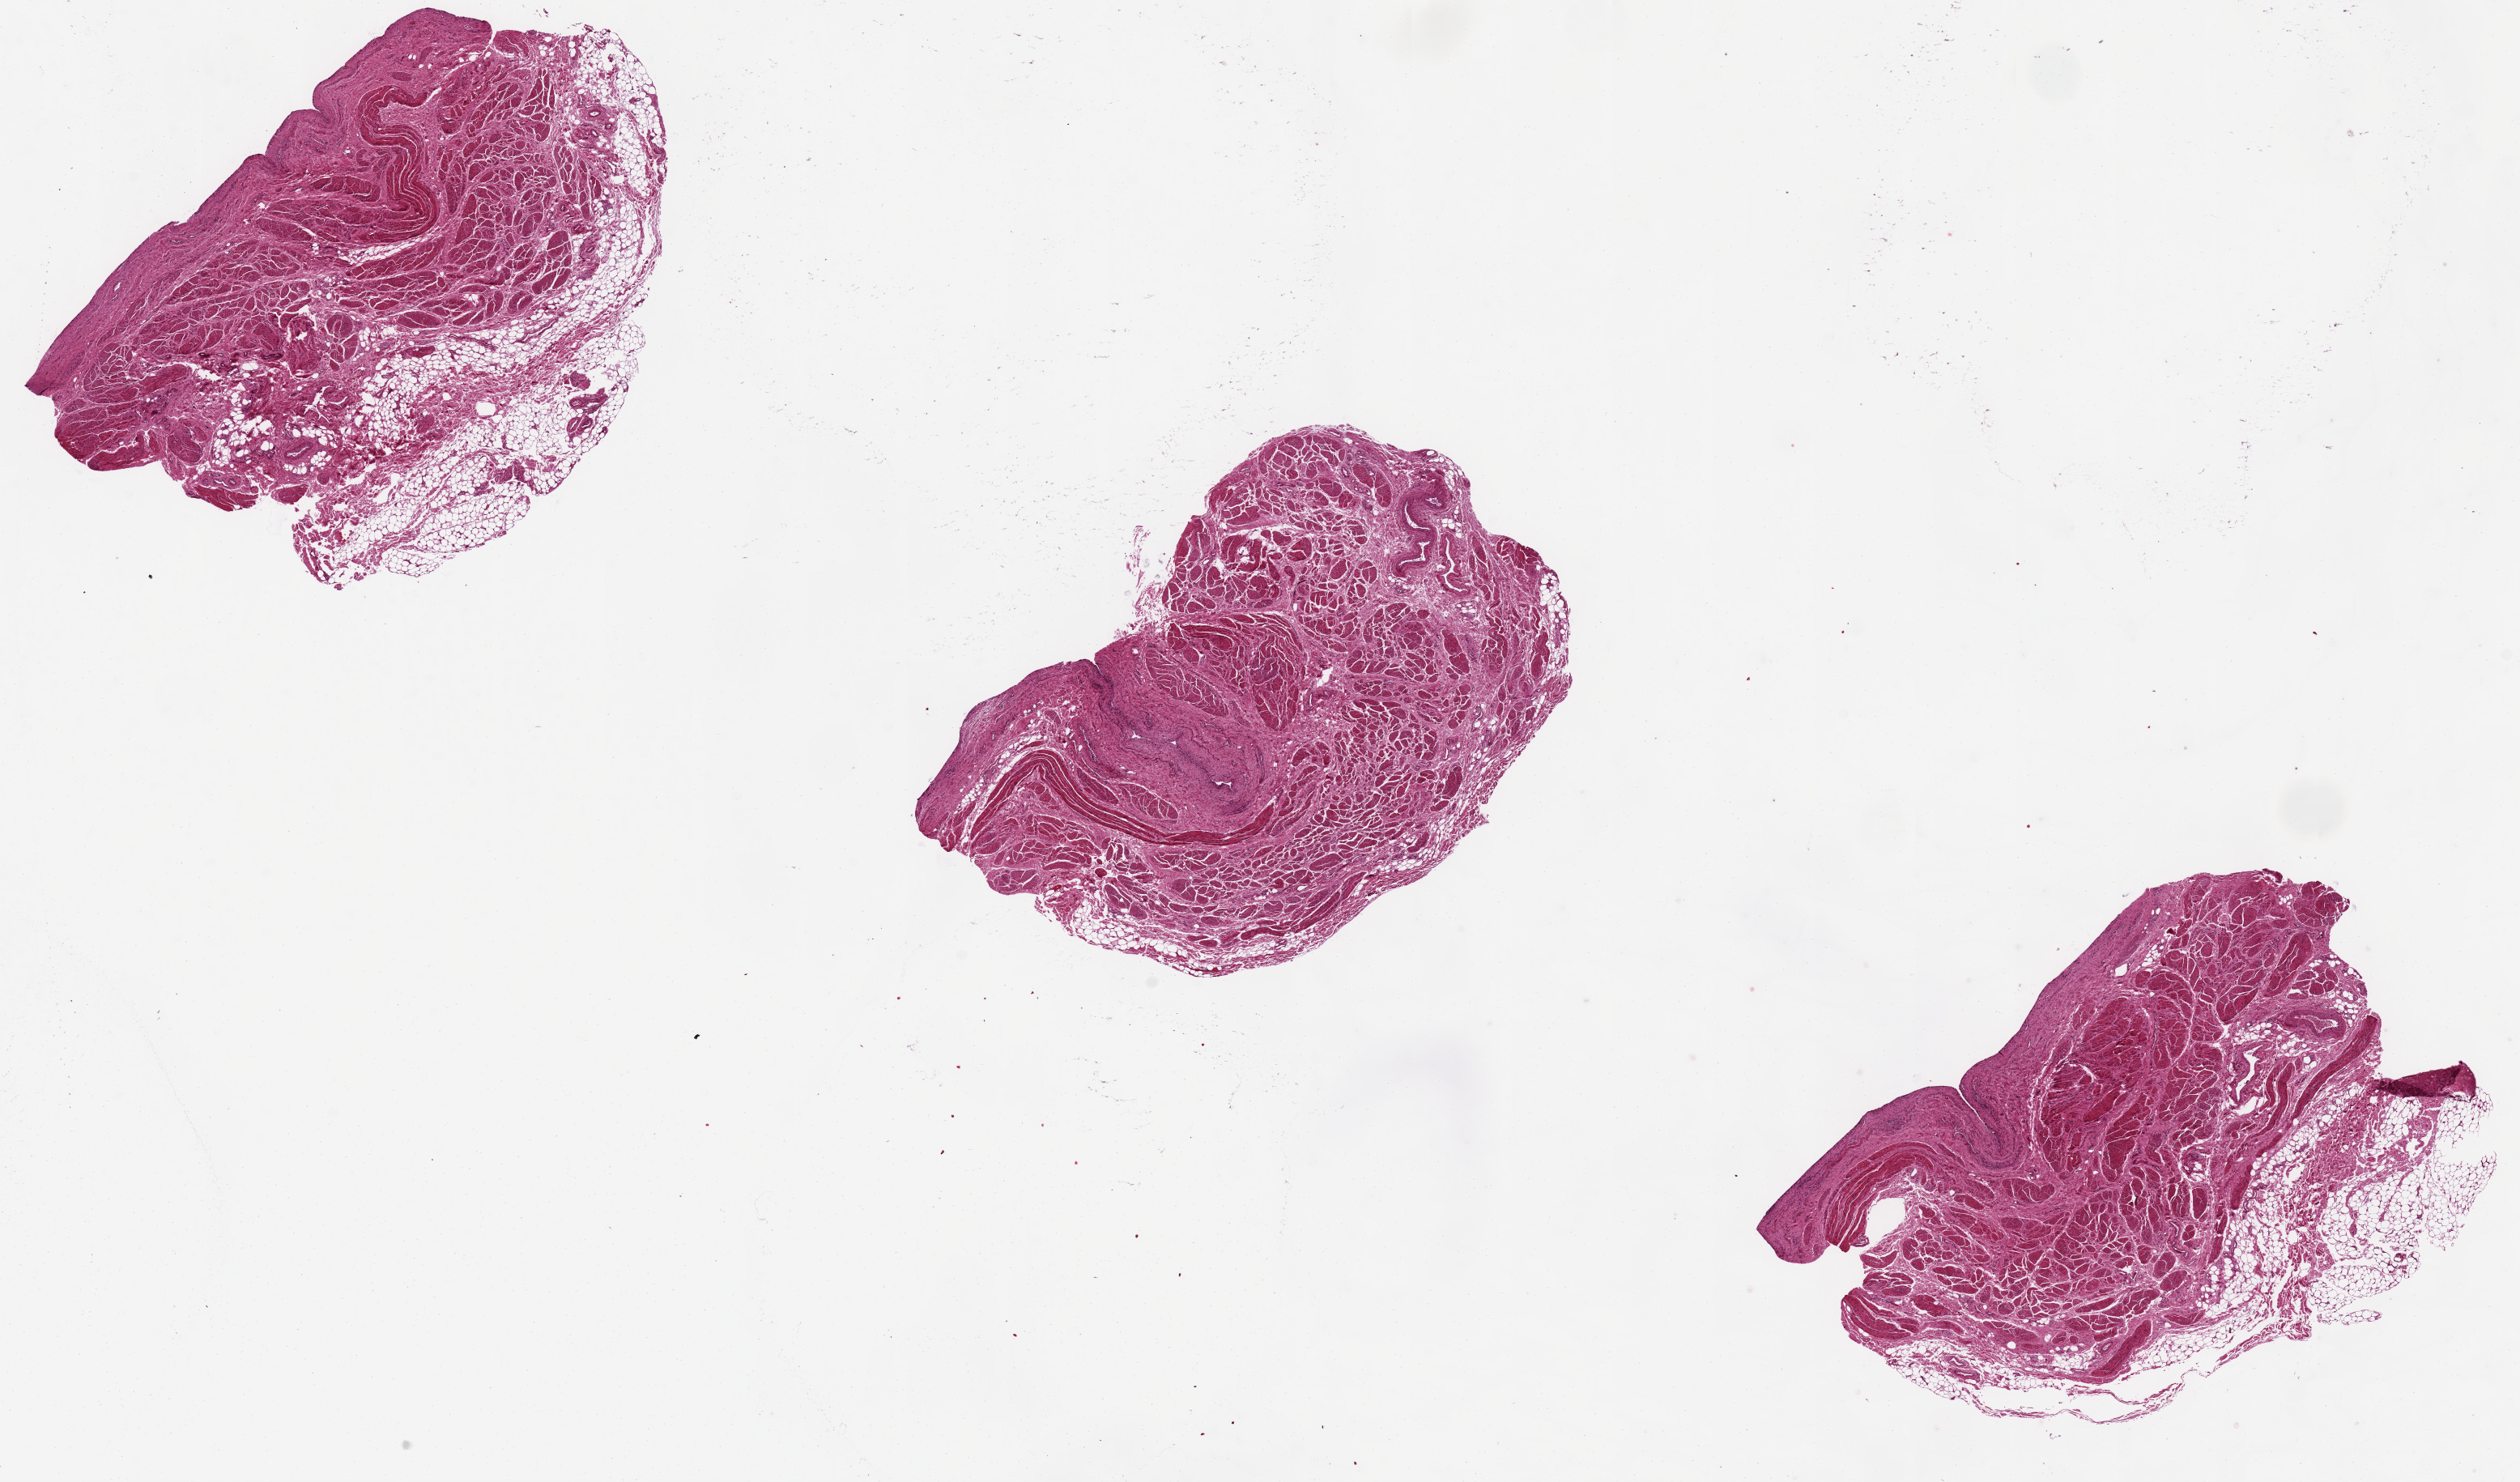
Digitized haematoxylin and eosin-stained section, brightfield — low-resolution overview of the scanned area, about 24.6 x 14.5 mm. PAXgene-fixed paraffin-embedded (PFPE) section. Section of urinary bladder (target tissue). Donor tissue sample. Donor sex: female.
Pathologist's review note for this sample: urothelium totally sloughed. Specimen thickness is ~4.3mm.